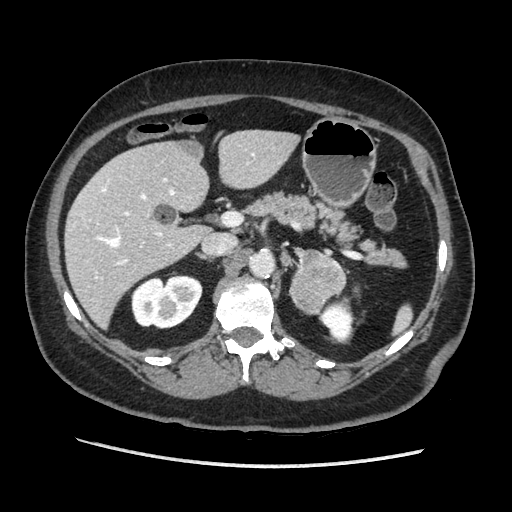
Contrast-enhanced abdominal CT, one axial slice; position 117 of 203 along the scan axis; soft-tissue window (W 400 / L 40 HU); 1.25 mm slice thickness; 512 × 512 image matrix. Female patient. From the clinical record (not read from this slice): diagnosis: adrenocortical carcinoma; tumour side: left adrenal; tumour size at pathology: 6.5 cm; Ki-67 index: 22 %; stage (as recorded): 2.
Annotated regions visible in this slice (semi-automatic segmentation, software-assisted and operator-edited):
- mass: bounding box (x1, y1, x2, y2) in pixels: (291, 250, 346, 312)